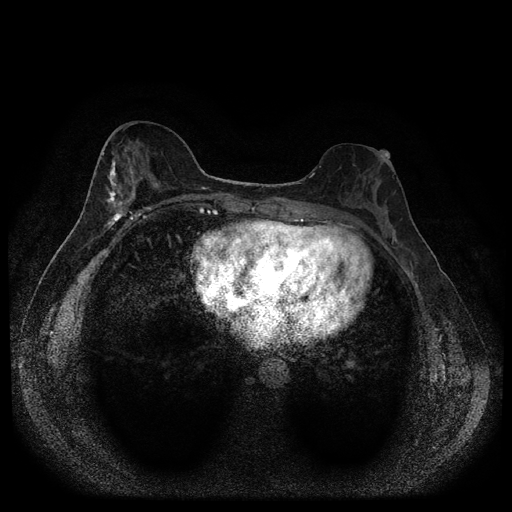
Breast MRI (dynamic contrast-enhanced, multi-phase), one axial slice. Dynamic contrast-enhanced series, time point 2 of 5 at this slice position (early post-contrast). 1.5 T. TE 2.7 ms, TR 5.4 ms. 2 mm slice thickness. 512 × 512 image matrix, field of view 330 × 330 mm. Female patient, age 49 years.
Structures marked on this image (semi-automatic segmentation, software-assisted and operator-edited):
- breast lesion (labelled 'tumour' in the annotation; benign lesions carry a separate 'benign' label): bounding box <104,157,121,212> (left, top, right, bottom; pixels)